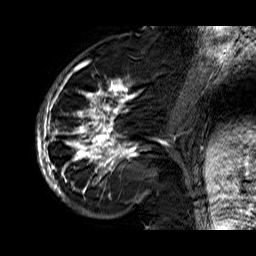
Breast MRI (dynamic contrast-enhanced), one sagittal slice. Slice 21 of 60 in the series (ordered by position). Dynamic contrast-enhanced series, time point 2 of 6 at this slice position (early post-contrast). 1.5 T. TE 6.3 ms, TR 32.9 ms. 4 mm slice thickness. 256 × 256 image matrix. Female patient. From the clinical record (not read from this slice): setting: breast cancer imaged before/during neoadjuvant chemotherapy; receptor status: HR-positive, HER2-negative.
Outlined on this slice (semi-automatic segmentation, software-assisted and operator-edited):
- analysis volume of interest (the breast-tissue region the enhancement analysis was run in; not a lesion): bounding box [x1, y1, x2, y2] px = [36, 74, 176, 210]
- tumour enhancement mask (voxels above the 100 % enhancement threshold inside the analysis volume of interest): [37, 74, 176, 202]